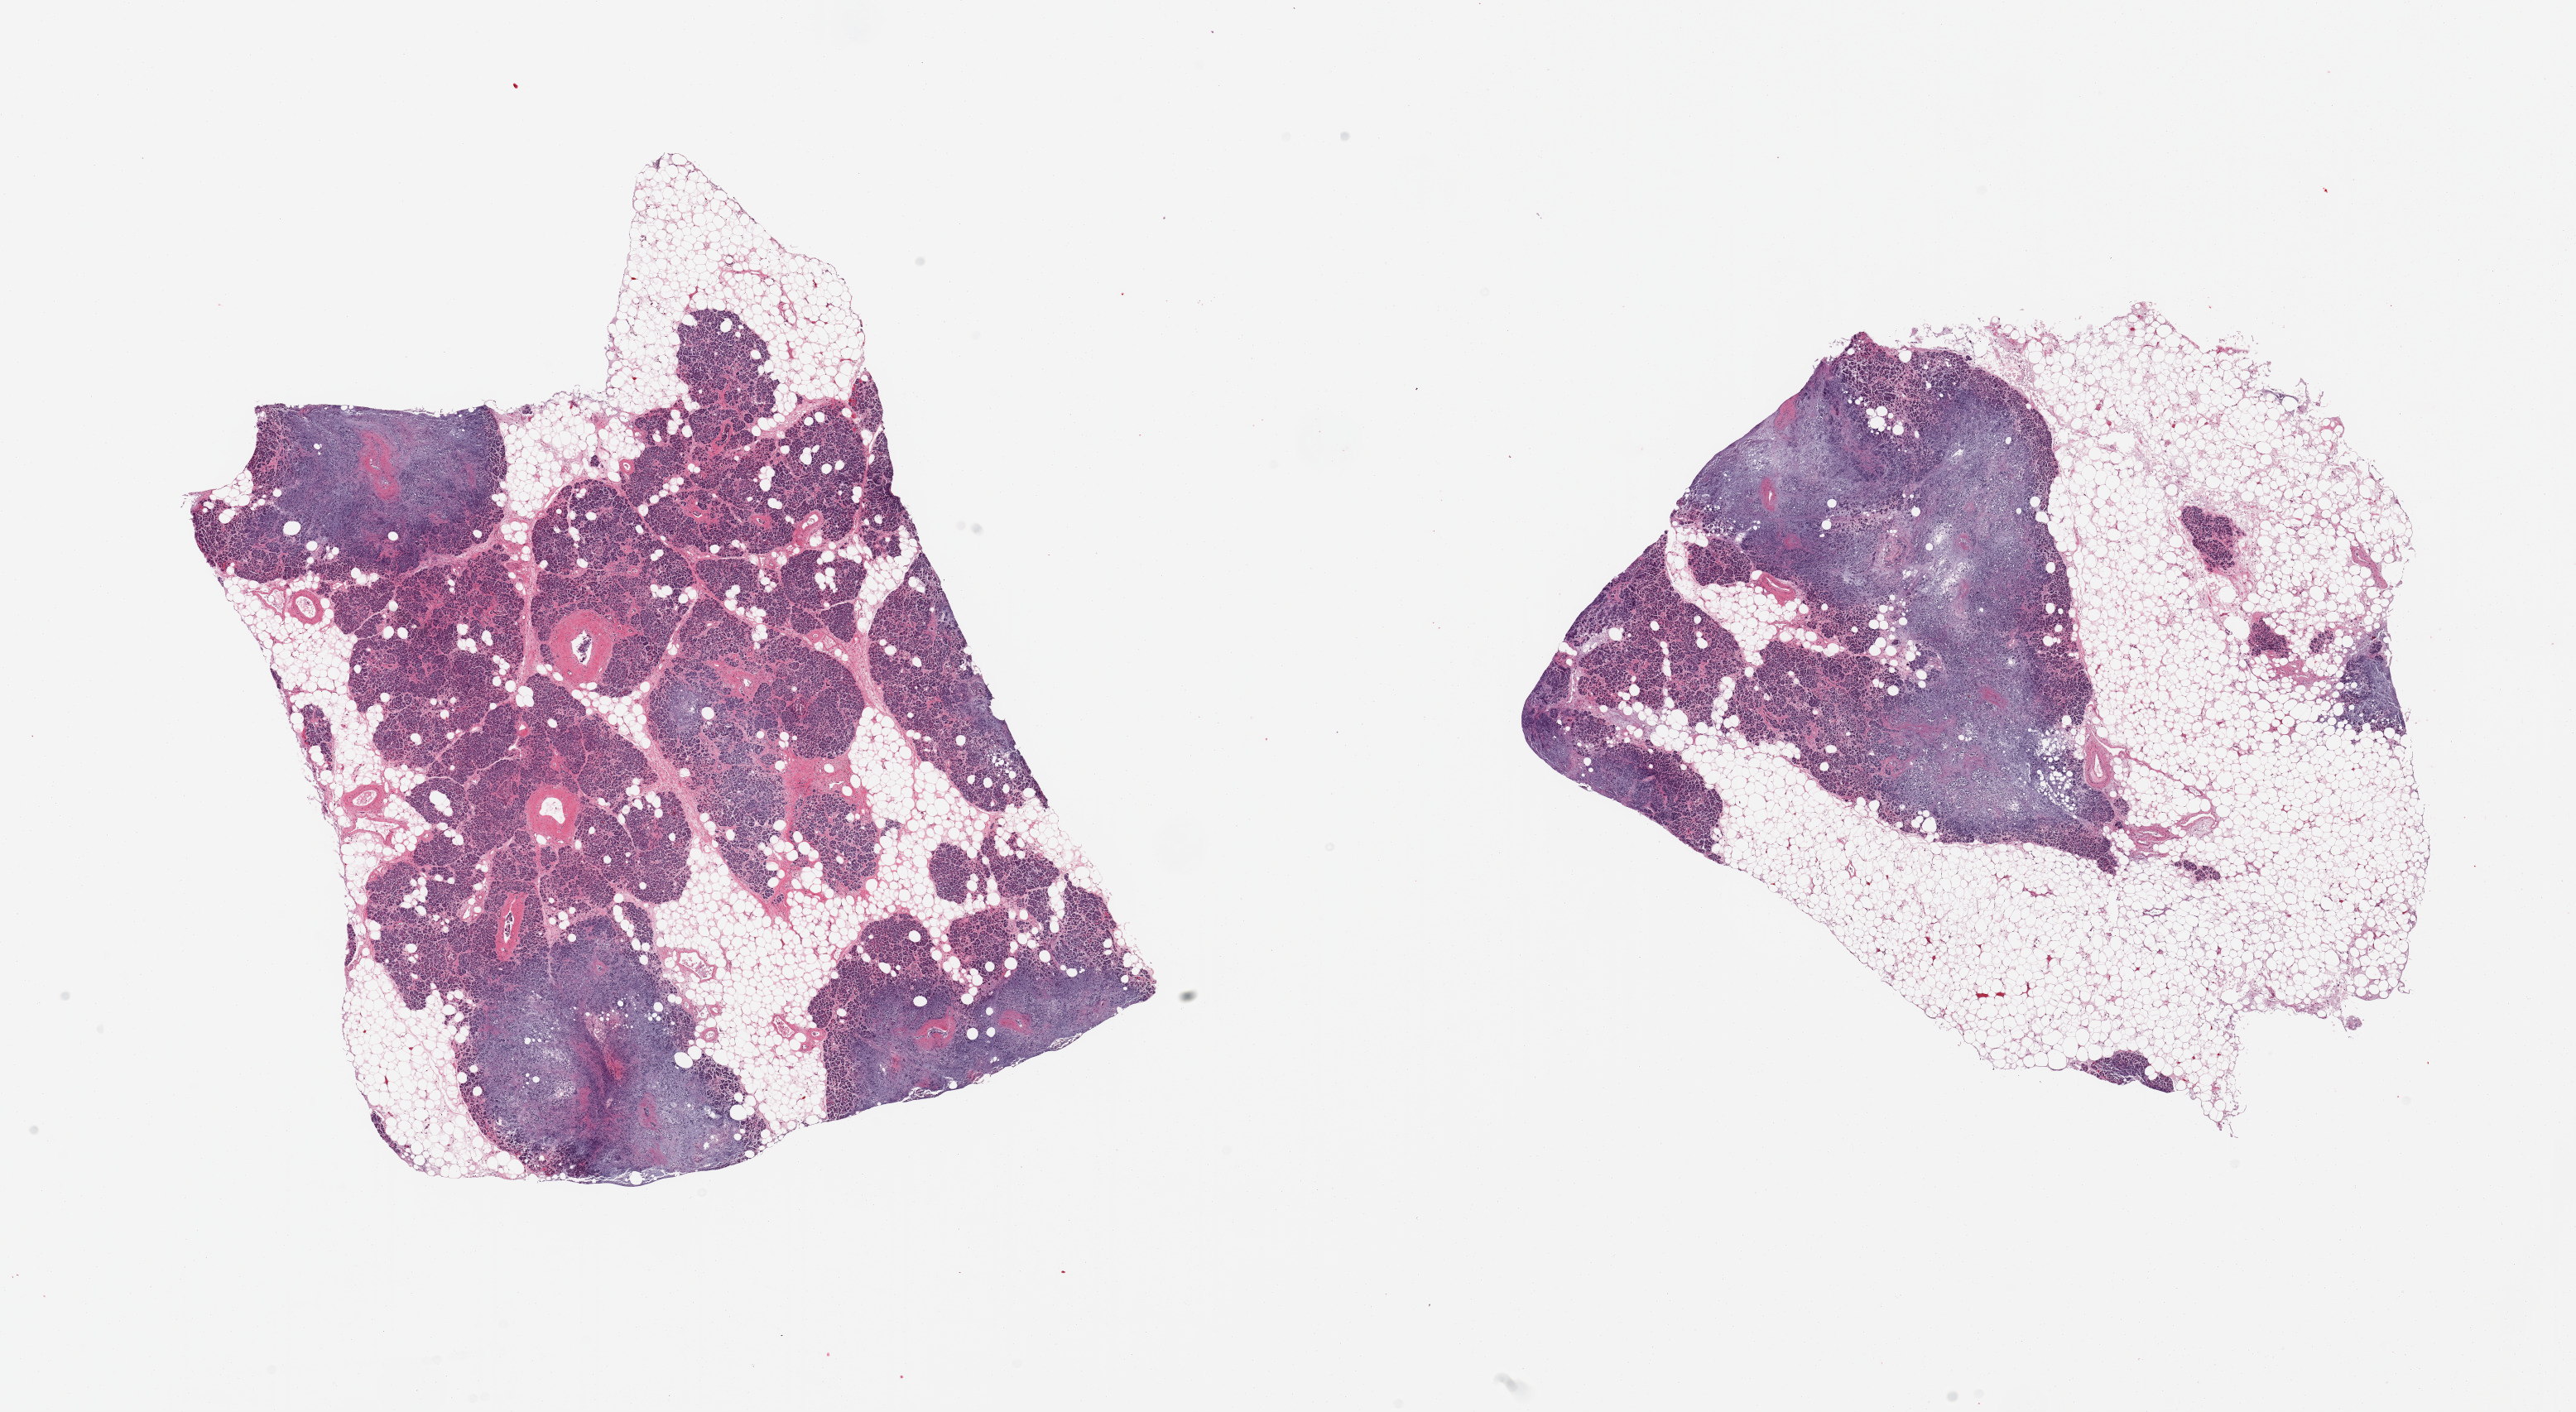
Whole-slide image, haematoxylin and eosin stain — shown as a low-resolution overview of the whole scanned area (about 24.6 x 13.5 mm, from a 20x scan). PAXgene-fixed paraffin-embedded (PFPE) section. Target tissue: pancreas. Tissue donor sample. Donor: male.
- review note (as recorded): 2 pieces; some areas have severe autolysis; high fat content: 60% & 40%; specimen has limited potential